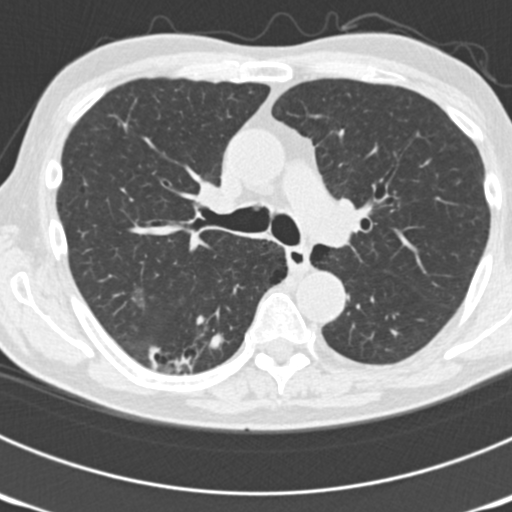
Axial slice from a low-dose chest CT screening exam. Third screening round (two years after baseline). Lung window (W 1500 / L -600 HU). 2 mm slice thickness. Standard (soft-tissue) reconstruction kernel (B30f). 512 × 512 image matrix, field of view 300 × 300 mm. Male, age 70 years at enrolment.
Lesion marked by an expert reader, bounding box (x1, y1, x2, y2) in pixels: (141, 314, 235, 386). The screening reader recorded 3 non-calcified nodules or masses ≥4 mm on this exam; which of them this box marks is not recorded. Official screen result: positive, other. Participant outcome: lung cancer diagnosed 14 days after this screen — bronchiolo-alveolar adenocarcinoma, NOS, right lower lobe, poorly differentiated (G3), stage IB (AJCC 6th edition), 30 mm at pathology.